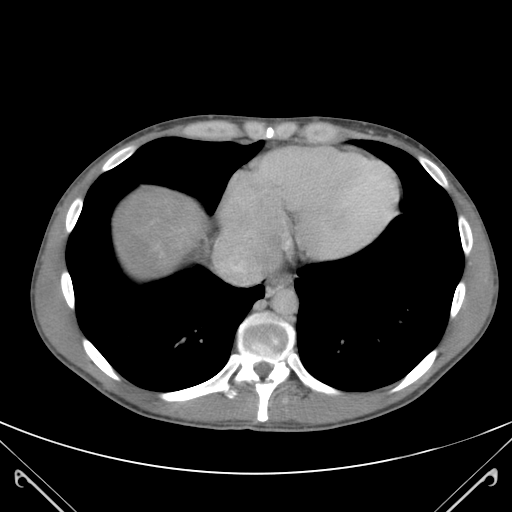
Contrast-enhanced abdominal CT (liver protocol), one axial slice. Position 109 of 118 along the scan axis. 120 kVp. Soft-tissue window (W 400 / L 40 HU). 512 × 512 image matrix, field of view 380 × 380 mm. Case-level facts recorded for this patient, not image findings: diagnosis: hepatocellular carcinoma (patient treated with transarterial chemoembolisation; whether this scan precedes or follows treatment is not stated here); TNM stage (as recorded): Stage-IIIB; Child-Pugh class: A.
Annotated regions visible in this slice (semi-automatic segmentation, software-assisted and operator-edited):
- abdominal aorta: bounding box <274,292,298,314> (left, top, right, bottom; pixels)
- liver parenchyma outside the tumour (the mass and vessels are separate outlines, so this box may not span the whole liver): <111,185,206,276>